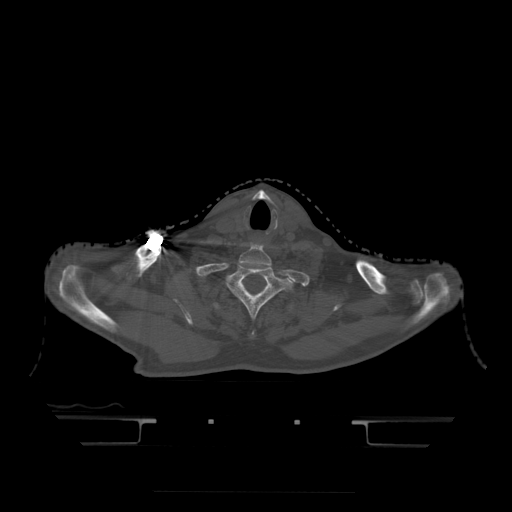
CT including the spine, one axial slice; position 399 of 522 along the scan axis; bone window (W 1800 / L 400 HU); 512 × 512 image matrix. Patient age 68 years. Case-level facts recorded for this patient, not image findings: primary cancer: urothelial.
Structures marked on this image (semi-automatic segmentation, software-assisted and operator-edited):
- T1 vertebra: bounding box <228,265,293,317> (left, top, right, bottom; pixels)
- T2 vertebra: <213,302,295,312>